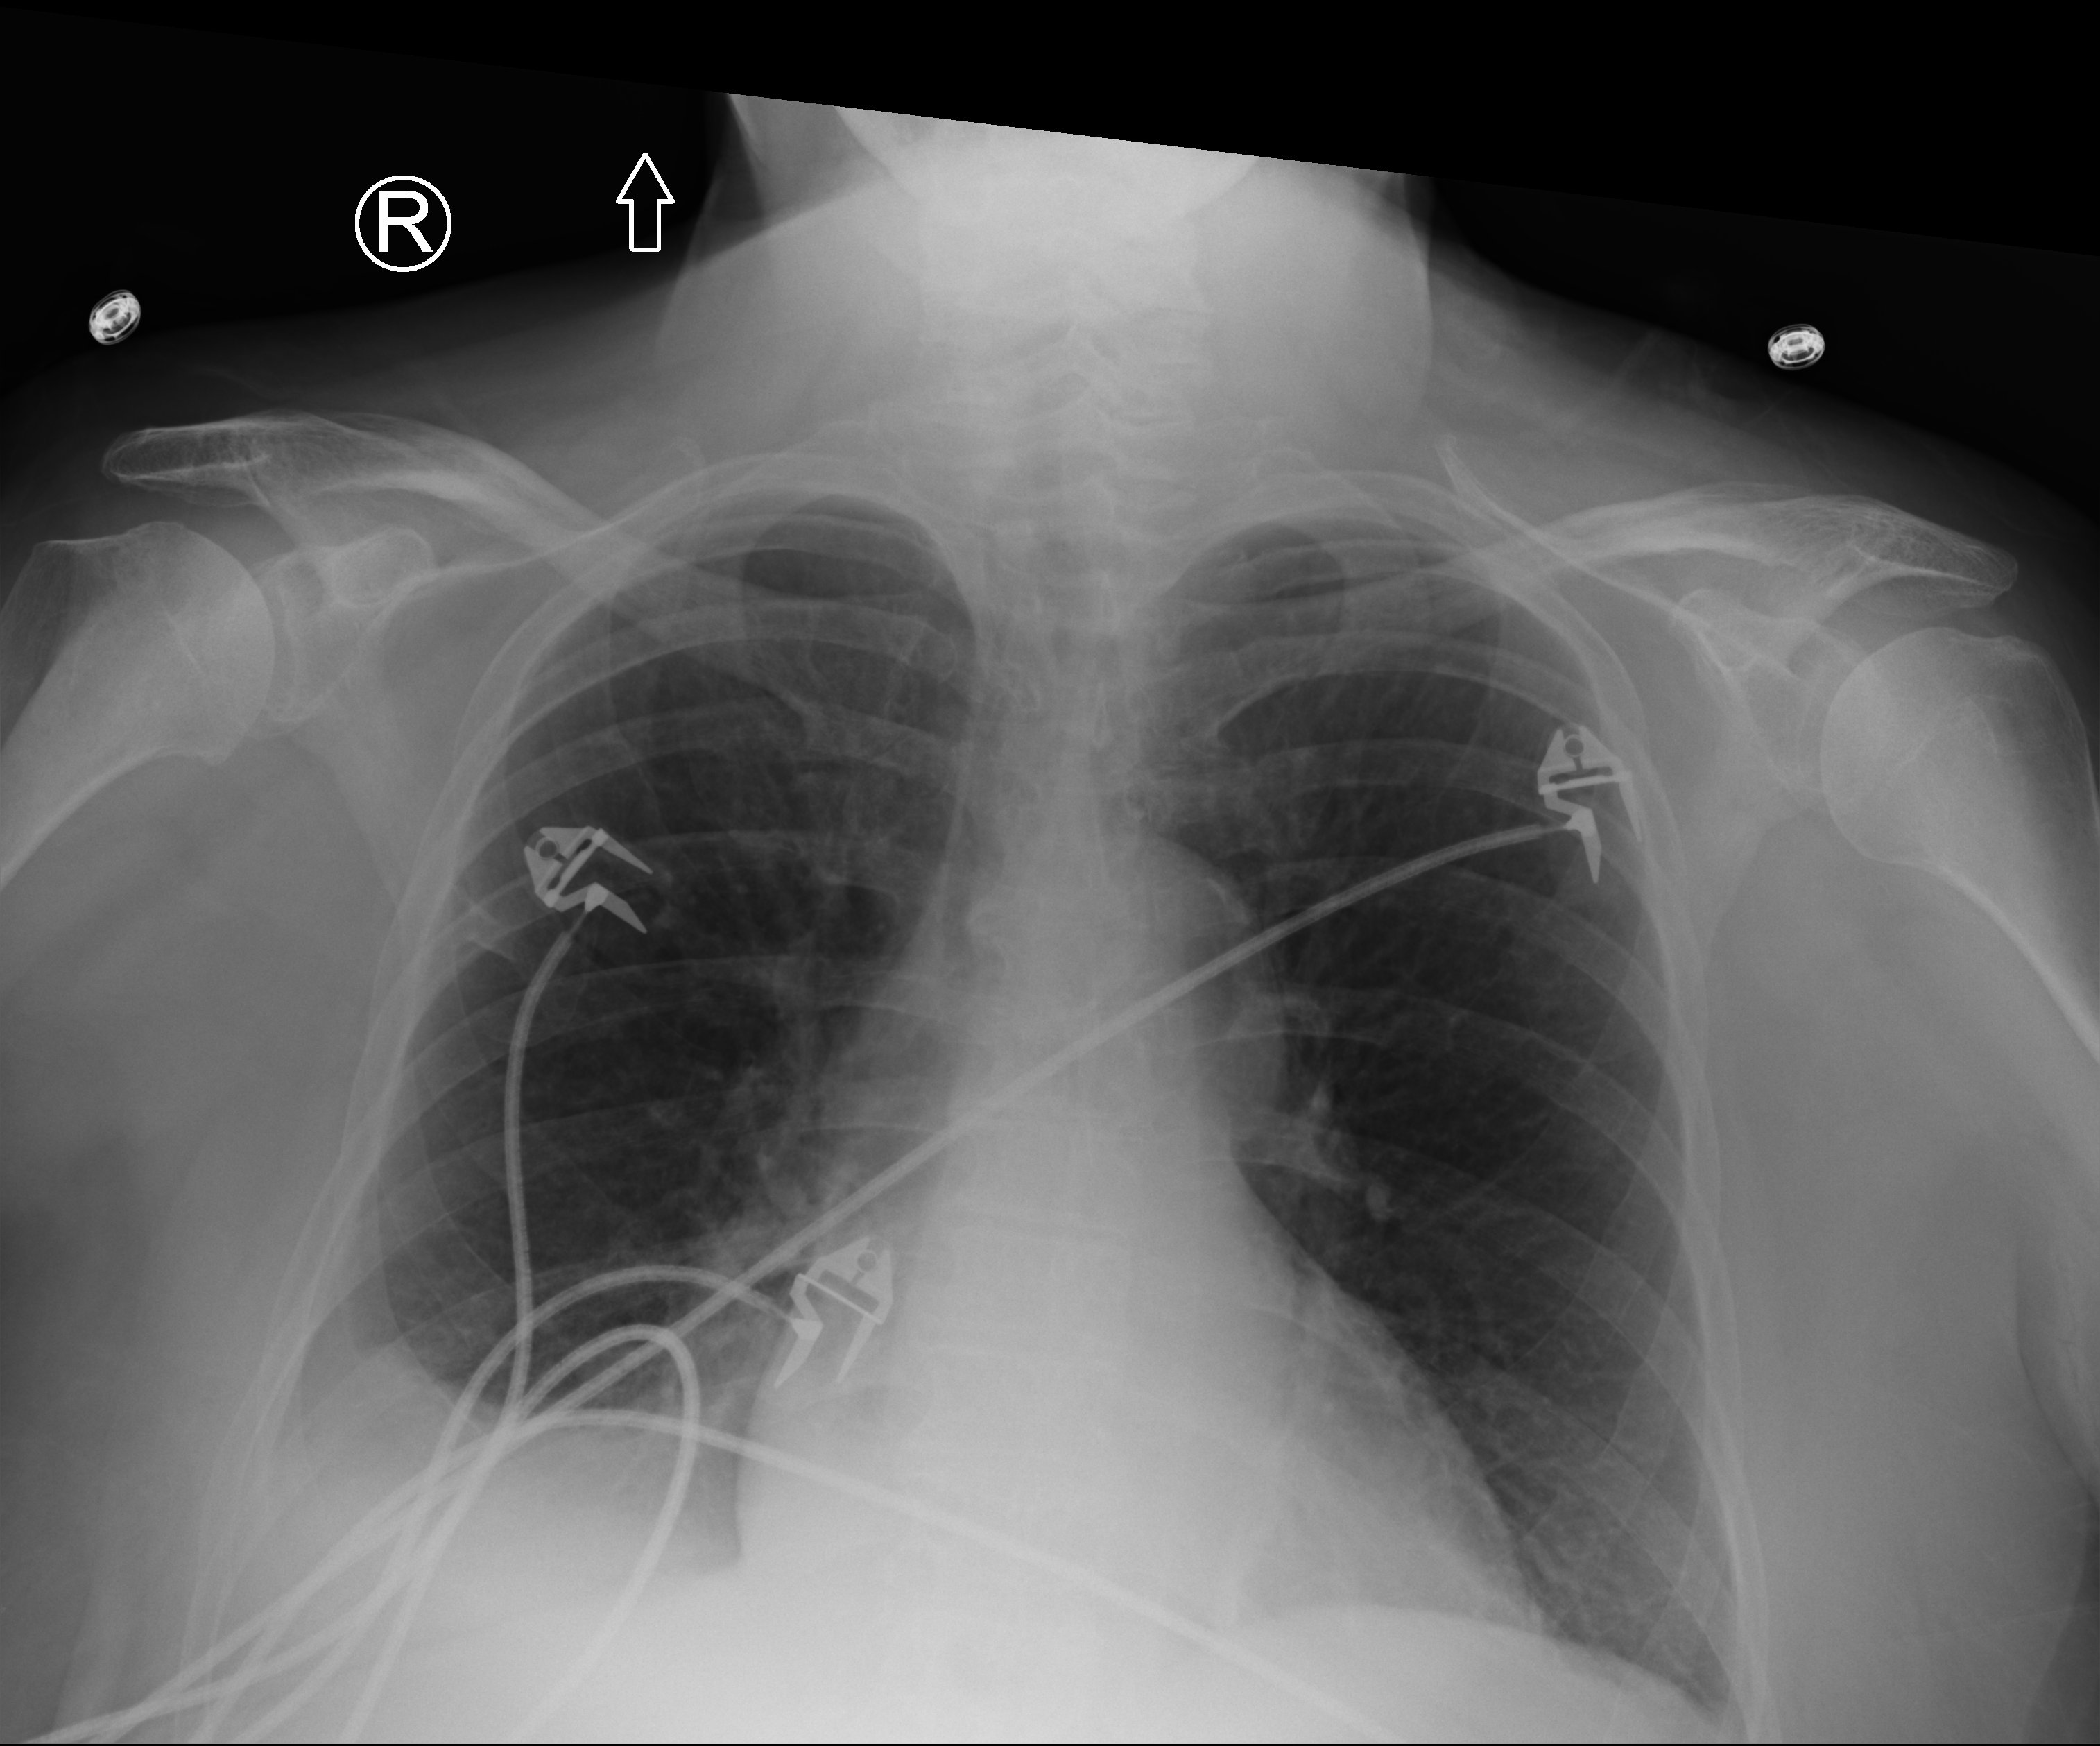
Bedside chest radiograph (computed radiography); anteroposterior (AP) projection. Female patient hospitalised with COVID-19, age 75–90 years.
Hospital-stay facts (about this admission, not read from this image; timing relative to this image not recorded): mechanically ventilated during this hospital stay: no; admitted to intensive care during this hospital stay: no.